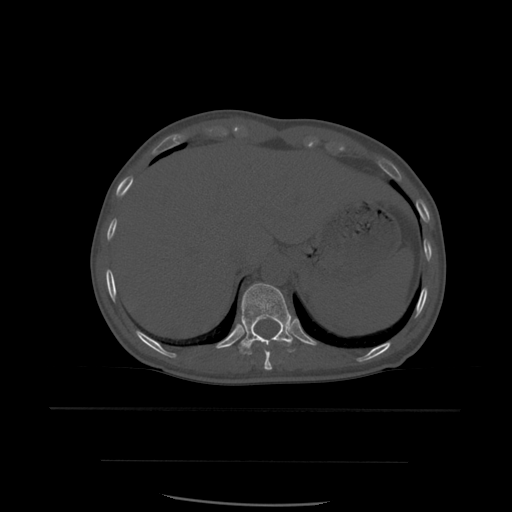
CT including the spine, one axial slice; position 300 of 574 along the scan axis; bone window (W 1800 / L 400 HU); 512 × 512 image matrix, field of view 392 × 392 mm. Patient age 48 years. From the clinical record (not read from this slice): primary cancer: lung; vertebrae with lytic lesions (as recorded): T11.
Structures marked on this image (semi-automatic segmentation, software-assisted and operator-edited):
- T10 vertebra: bounding box (x1, y1, x2, y2) in pixels: (264, 341, 290, 371)
- T11 vertebra: (240, 283, 298, 355)